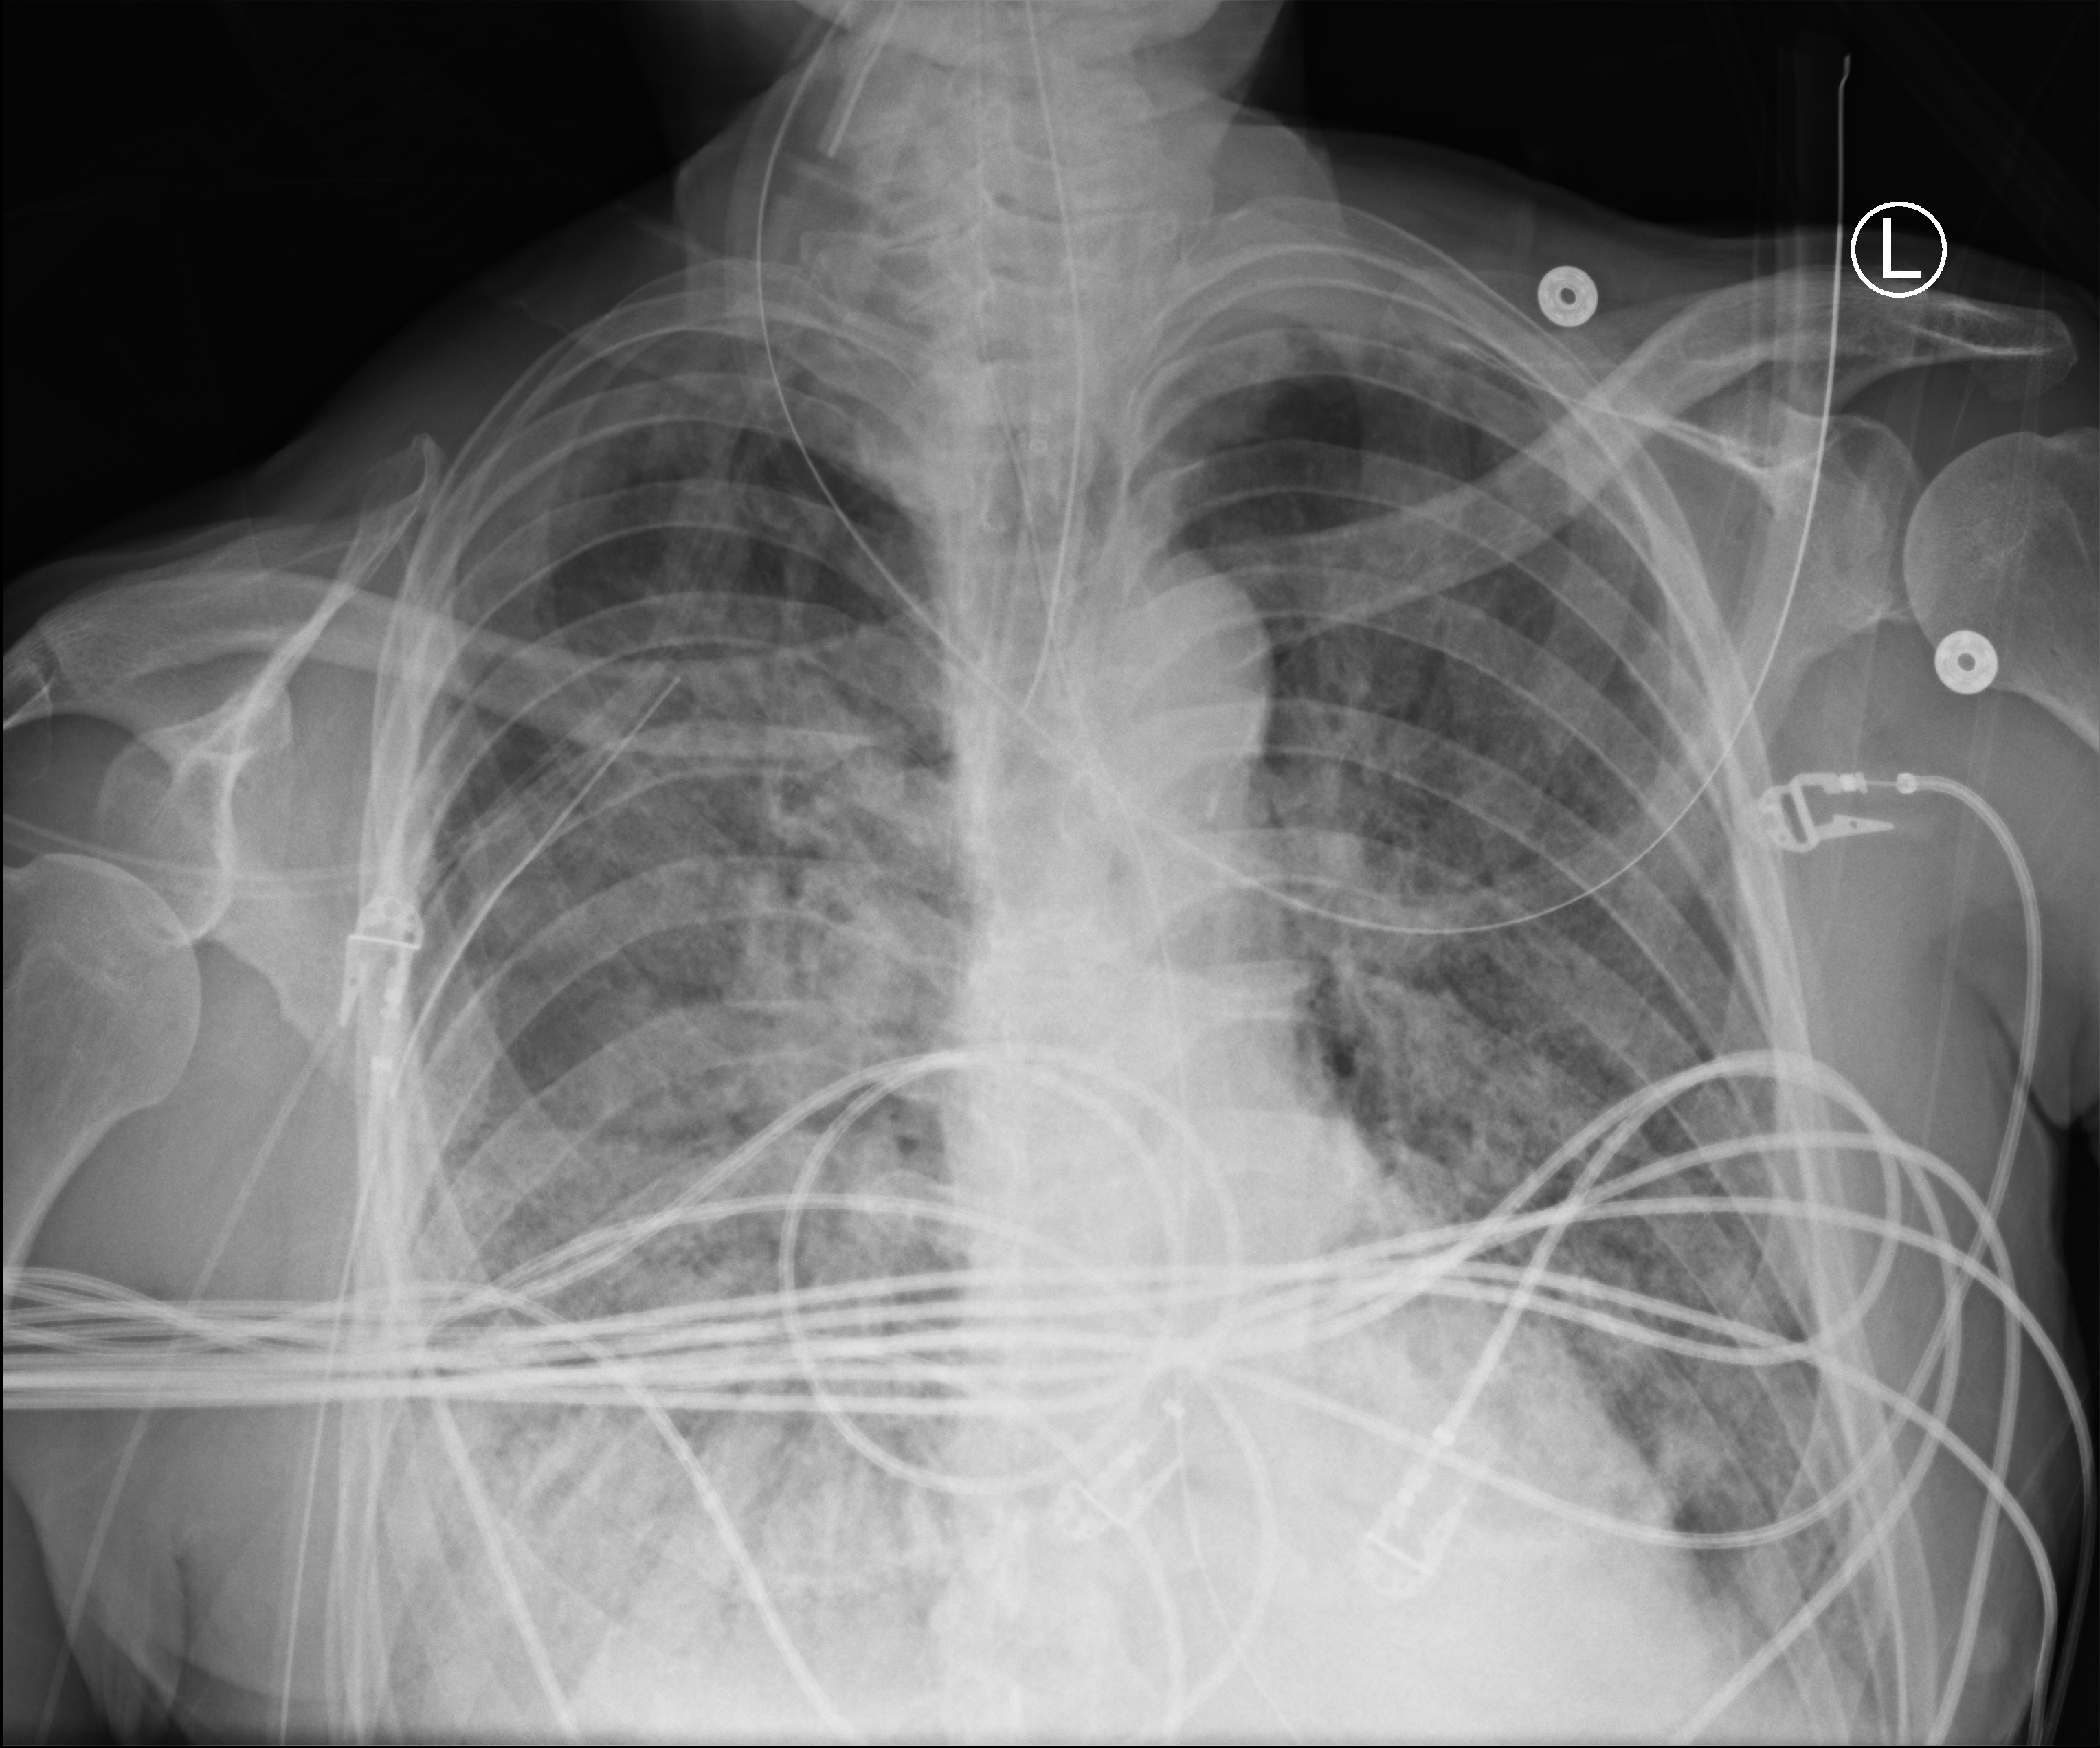
Chest X-ray (portable); anteroposterior (AP) projection. Male patient hospitalised with COVID-19, age 60–74 years.
From the hospital-stay record, not from the radiograph (when in the stay this image was taken is not recorded):
- chronic kidney disease (admission record): no